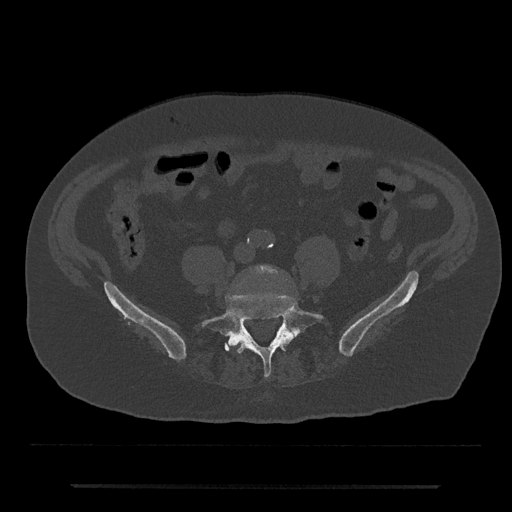
CT including the spine, one axial slice. Slice 299 of 797 in the series (ordered by position). 120 kVp. Bone window (W 1800 / L 400 HU). 0.5 mm slice thickness. 512 × 512 image matrix, field of view 434 × 434 mm. Male patient, age 80 years. From the clinical record (not read from this slice): primary cancer: prostate; vertebrae with lytic lesions (as recorded): L1, T11.
Annotated regions visible in this slice (semi-automatic segmentation, software-assisted and operator-edited):
- L4 vertebra: bounding box (x1, y1, x2, y2) in pixels: (251, 265, 278, 274)
- L5 vertebra: (201, 293, 323, 377)